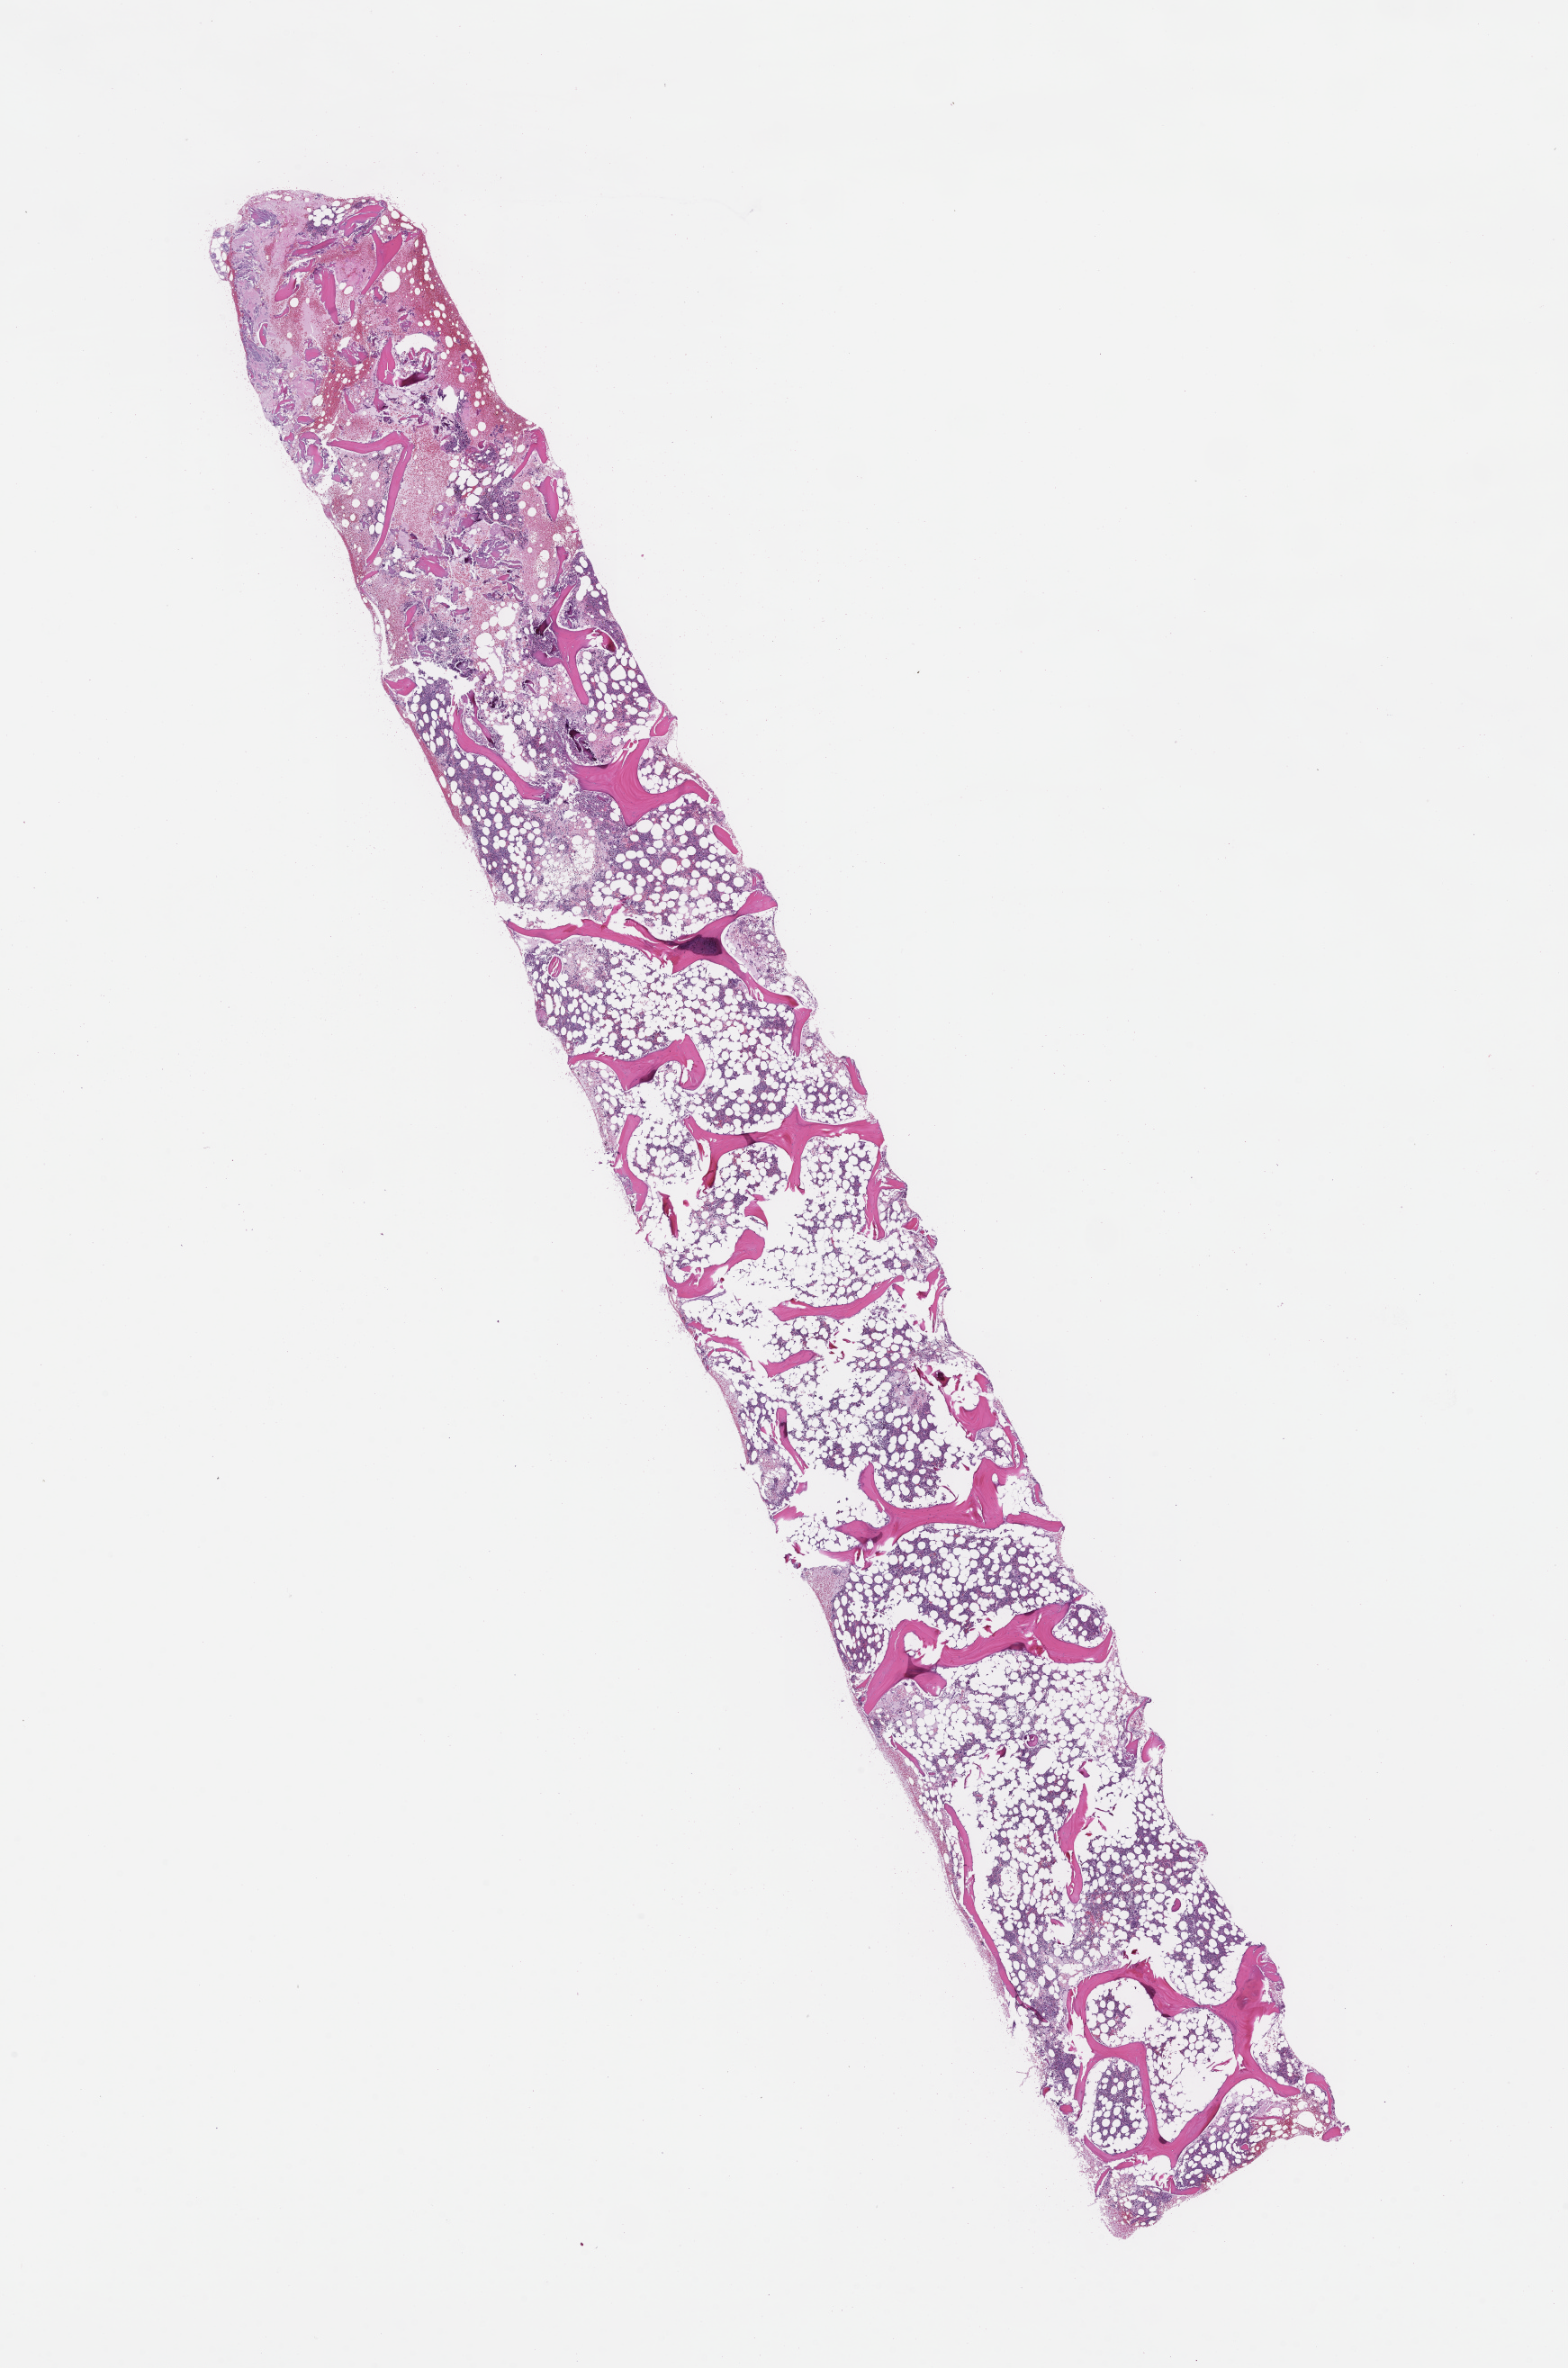
Whole-slide image, haematoxylin and eosin stain — shown as a low-resolution overview of the whole scanned area (about 14.1 x 21.3 mm); formalin-fixed, paraffin-embedded (FFPE) tissue; site: bone marrow; specimen time point: archival tissue. Patient: female.
This section: primary tumor. Diagnosis: Plasma Cell Myeloma.